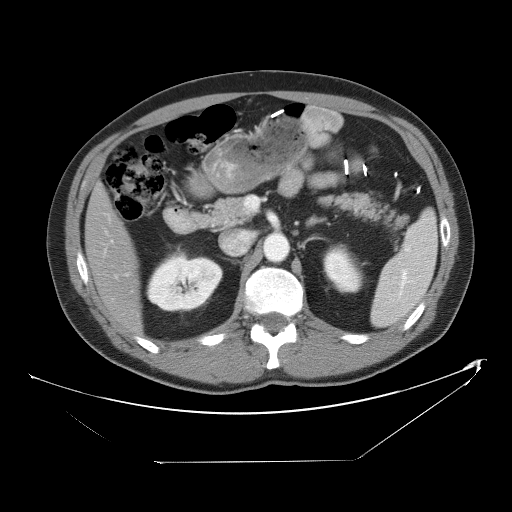
Contrast-enhanced abdominal CT, one axial slice. Slice 26 of 53 in the series (ordered by position). Reconstruction kernel STANDARD. Soft-tissue window (W 400 / L 40 HU). 5 mm slice thickness. 512 × 512 image matrix, field of view 438 × 438 mm. Male patient, age 59 years. Case-level facts recorded for this patient, not image findings: diagnosis: colorectal cancer liver metastases, imaged before liver resection; multiple liver metastases: yes; largest metastasis: 8.5 cm.
Structures marked on this image (outlined manually by an expert reader):
- hepatic veins: bounding box (x1, y1, x2, y2) in pixels: (106, 214, 118, 278)
- liver: (86, 189, 140, 332)
- planned liver remnant (the part of the liver to remain after resection): (86, 188, 140, 332)
- portal vein (with intrahepatic branches): (106, 232, 113, 242)